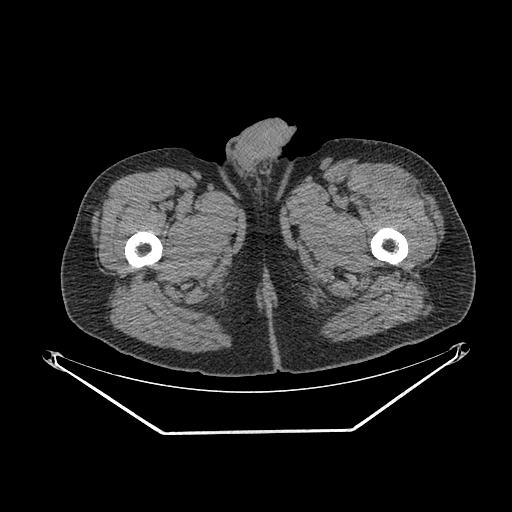
CT of an extremity soft-tissue mass (from a PET/CT study), one axial slice; position 262 of 267 along the scan axis; reconstruction kernel SOFT; 140 kVp; soft-tissue window (W 400 / L 40 HU); 512 × 512 image matrix, field of view 500 × 500 mm. Male patient. From the clinical record (not read from this slice): histological type: extraskeletal osteosarcoma; grade: high; site of the primary tumour: thigh.
Annotated regions visible in this slice (expert contour drawn on MRI and transferred to this co-registered scan by the dataset authors):
- gross tumour volume (mass): bounding box (x1, y1, x2, y2) in pixels: (411, 183, 417, 193)